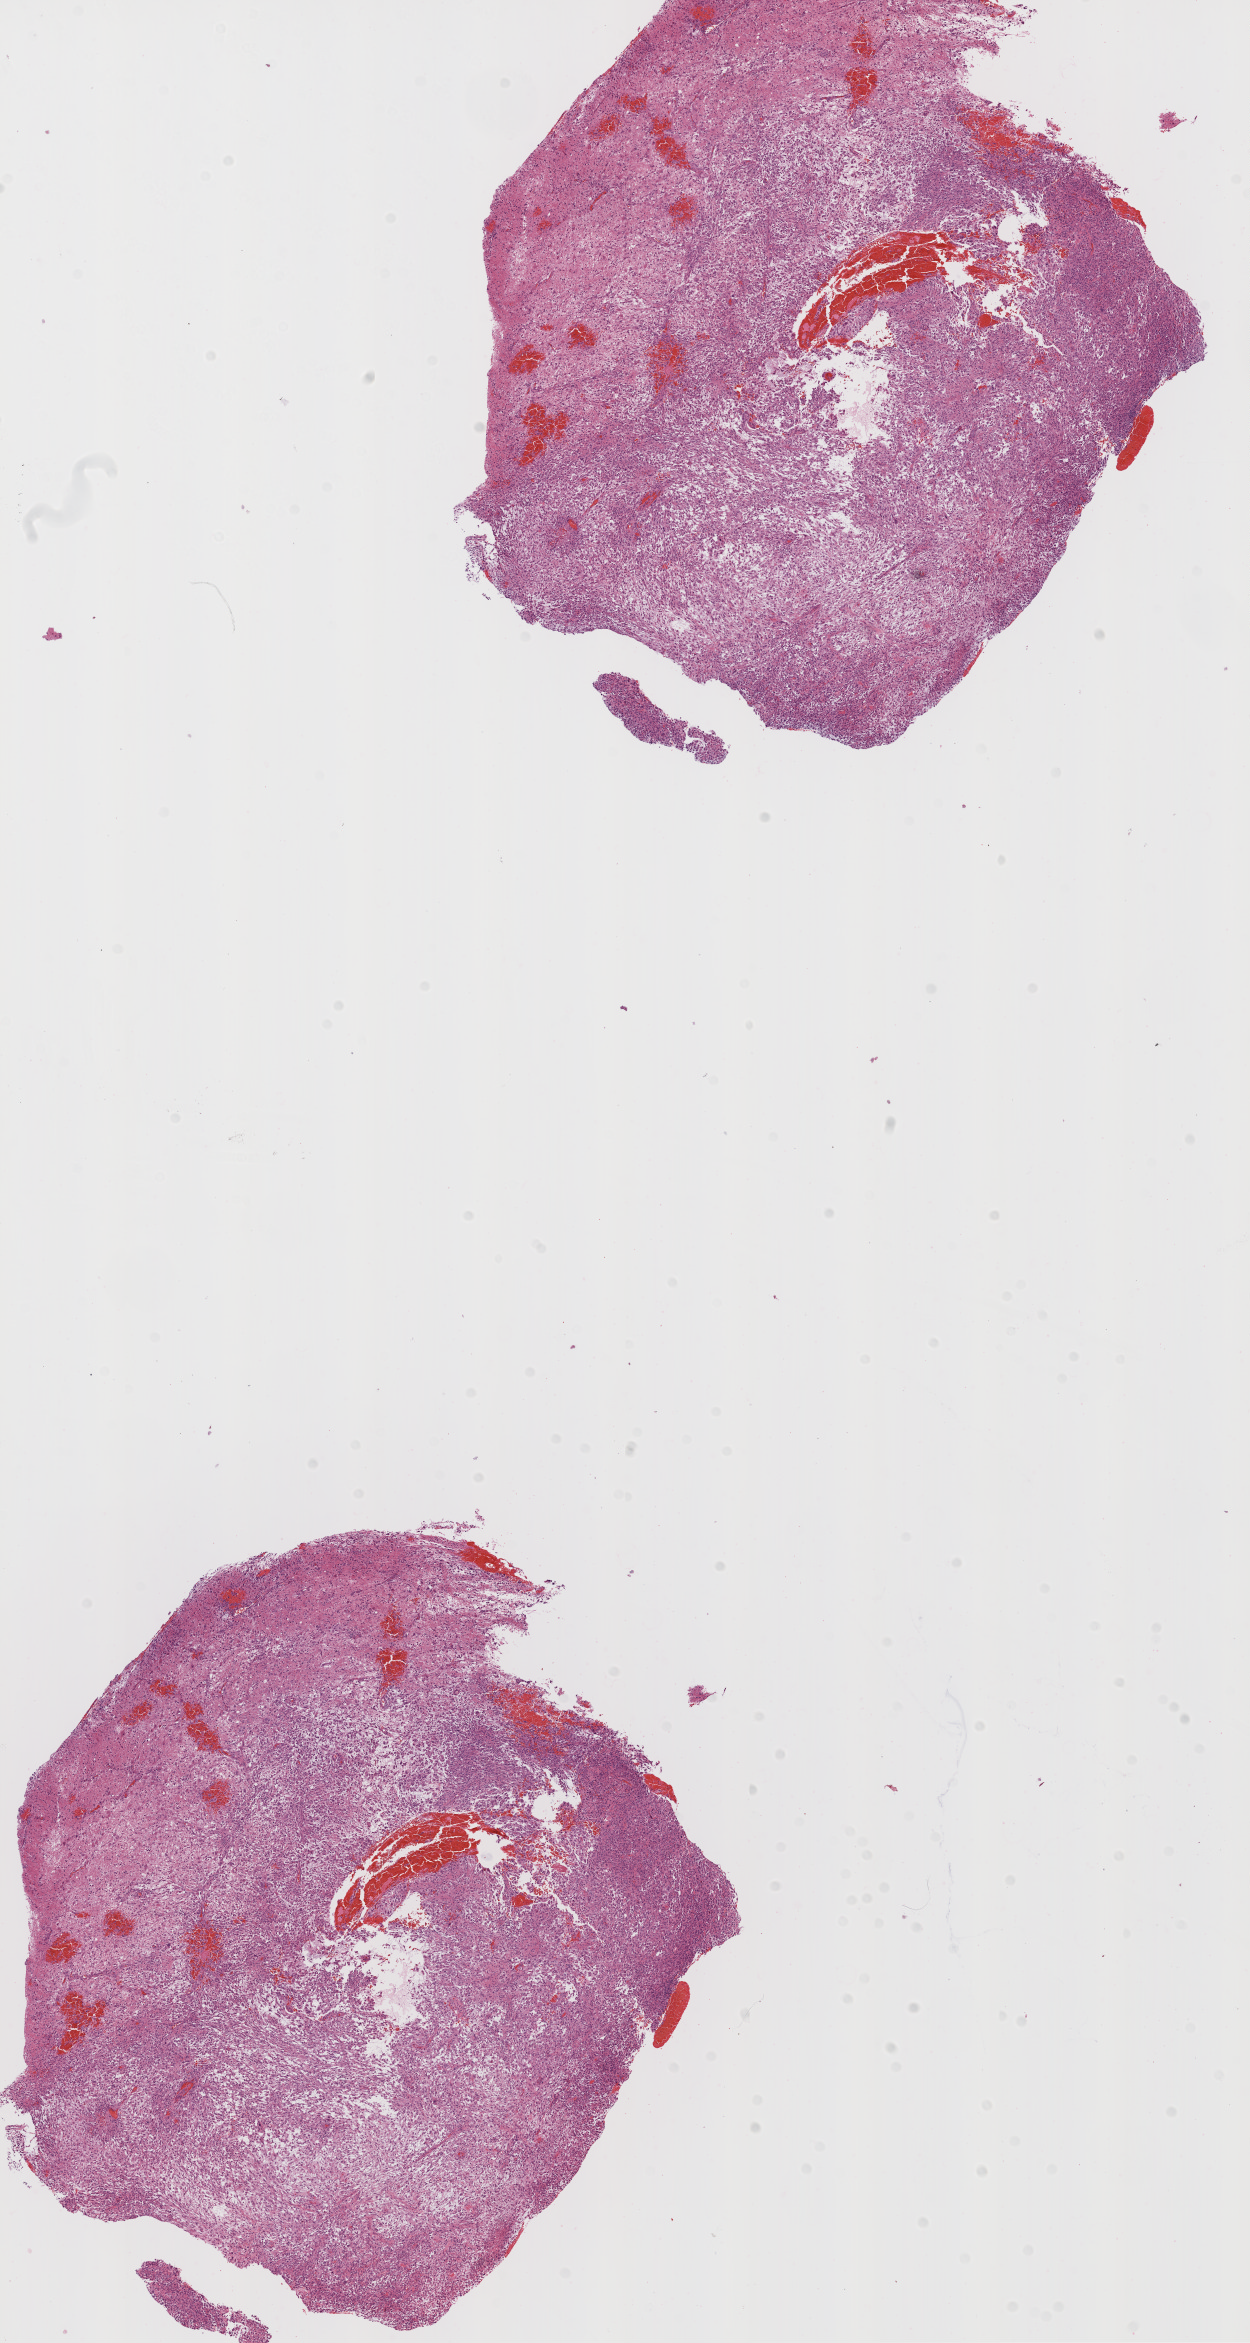
Digitized H&E tissue section (whole slide) — a low-resolution overview of the entire scanned area, about 10.0 x 18.8 mm; formalin-fixed paraffin-embedded (FFPE) diagnostic section; primary tumour sample from the brain. Male patient; age at initial diagnosis 54 years.
• pathologic diagnosis: Glioblastoma